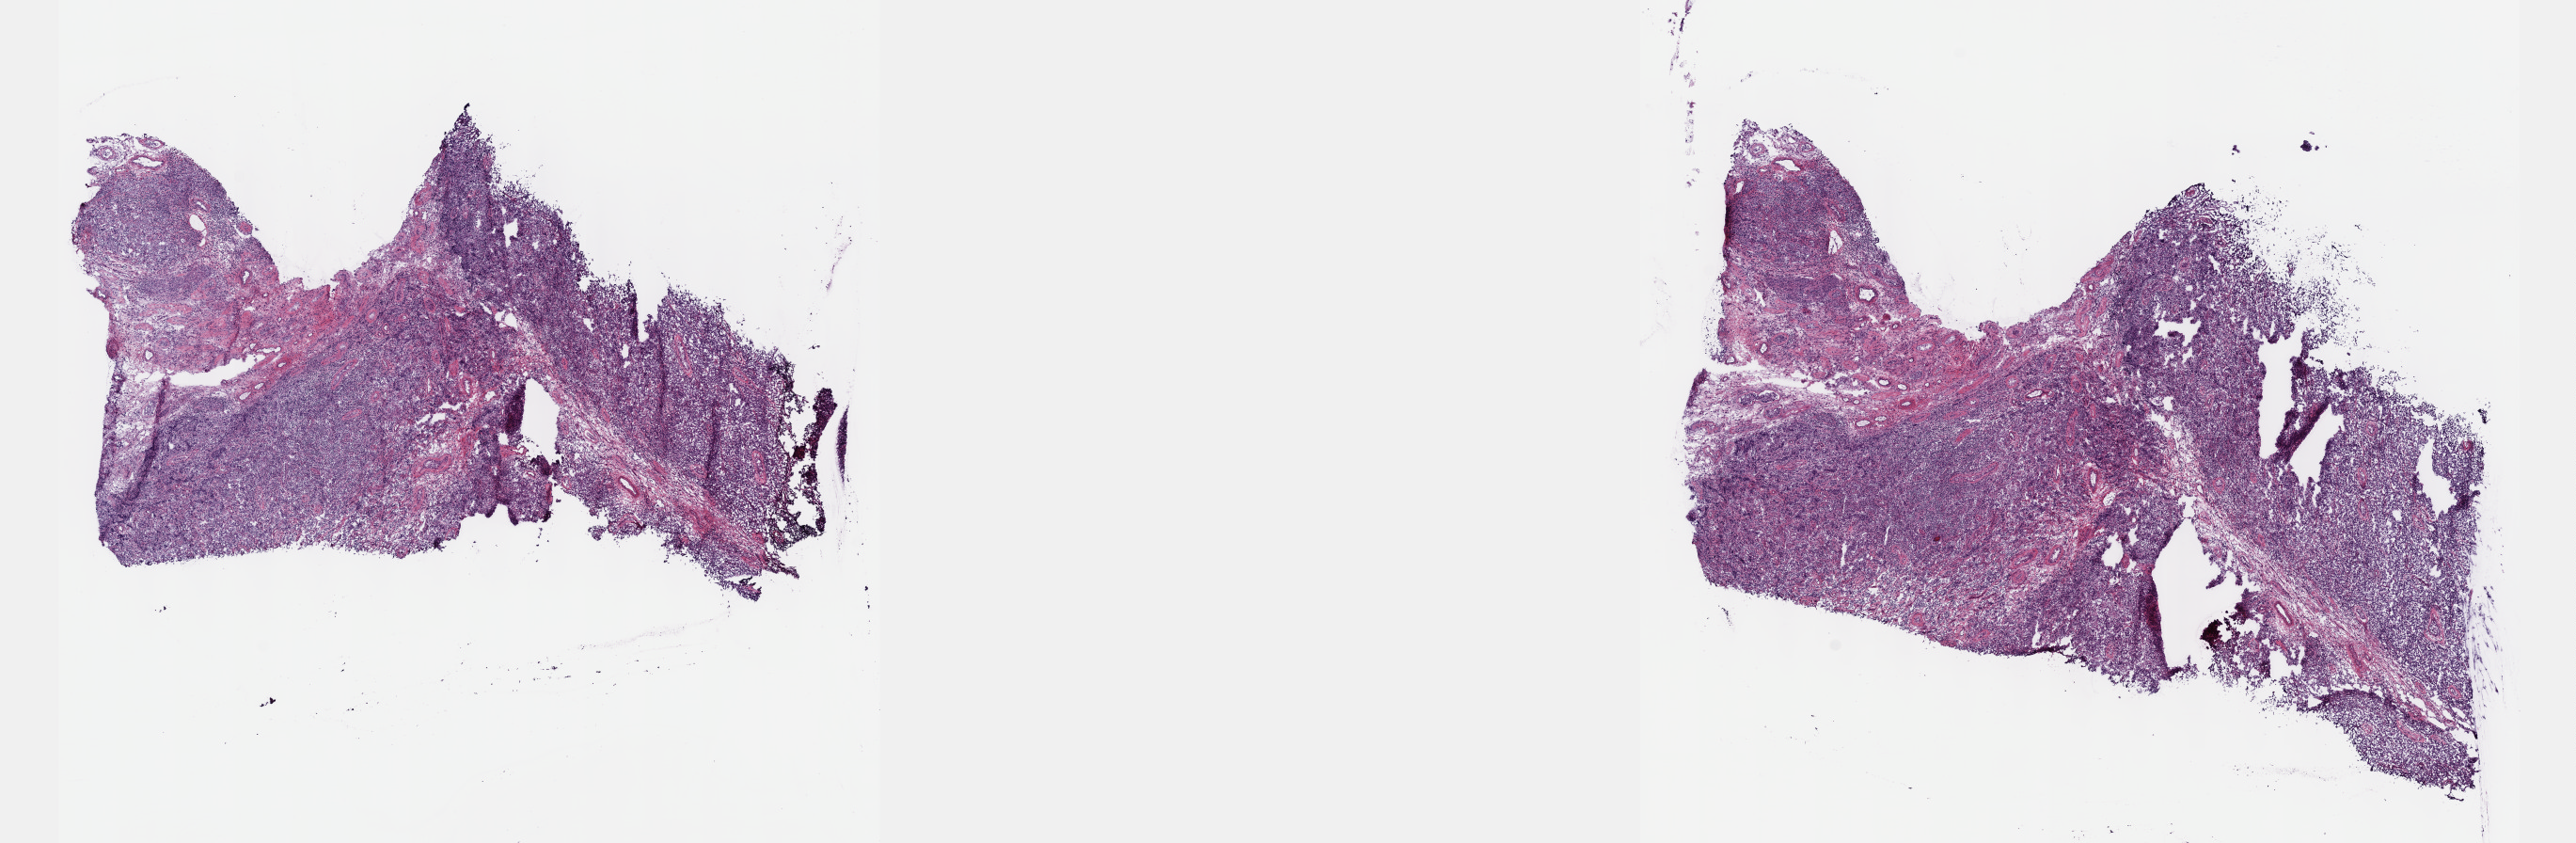
Whole-slide histology image, H&E-stained, shown as a low-resolution overview of the whole scanned area (about 22.1 x 7.2 mm, acquisition: 40x scan), frozen section from the top of the tissue portion, primary tumour sample from the testis. Male patient; age at initial diagnosis 26 years. Slide review estimates, as recorded: tumour cells 70%, tumour nuclei 70%, normal cells 0%, stromal cells 25%, necrosis 5%. Inflammatory infiltration, as recorded: lymphocyte infiltration 40%, monocyte infiltration 20%, neutrophil infiltration 20%.
TNM: T2 N0 M0. AJCC pathologic stage: IA (7th edition). Histologic diagnosis: Seminoma, NOS.